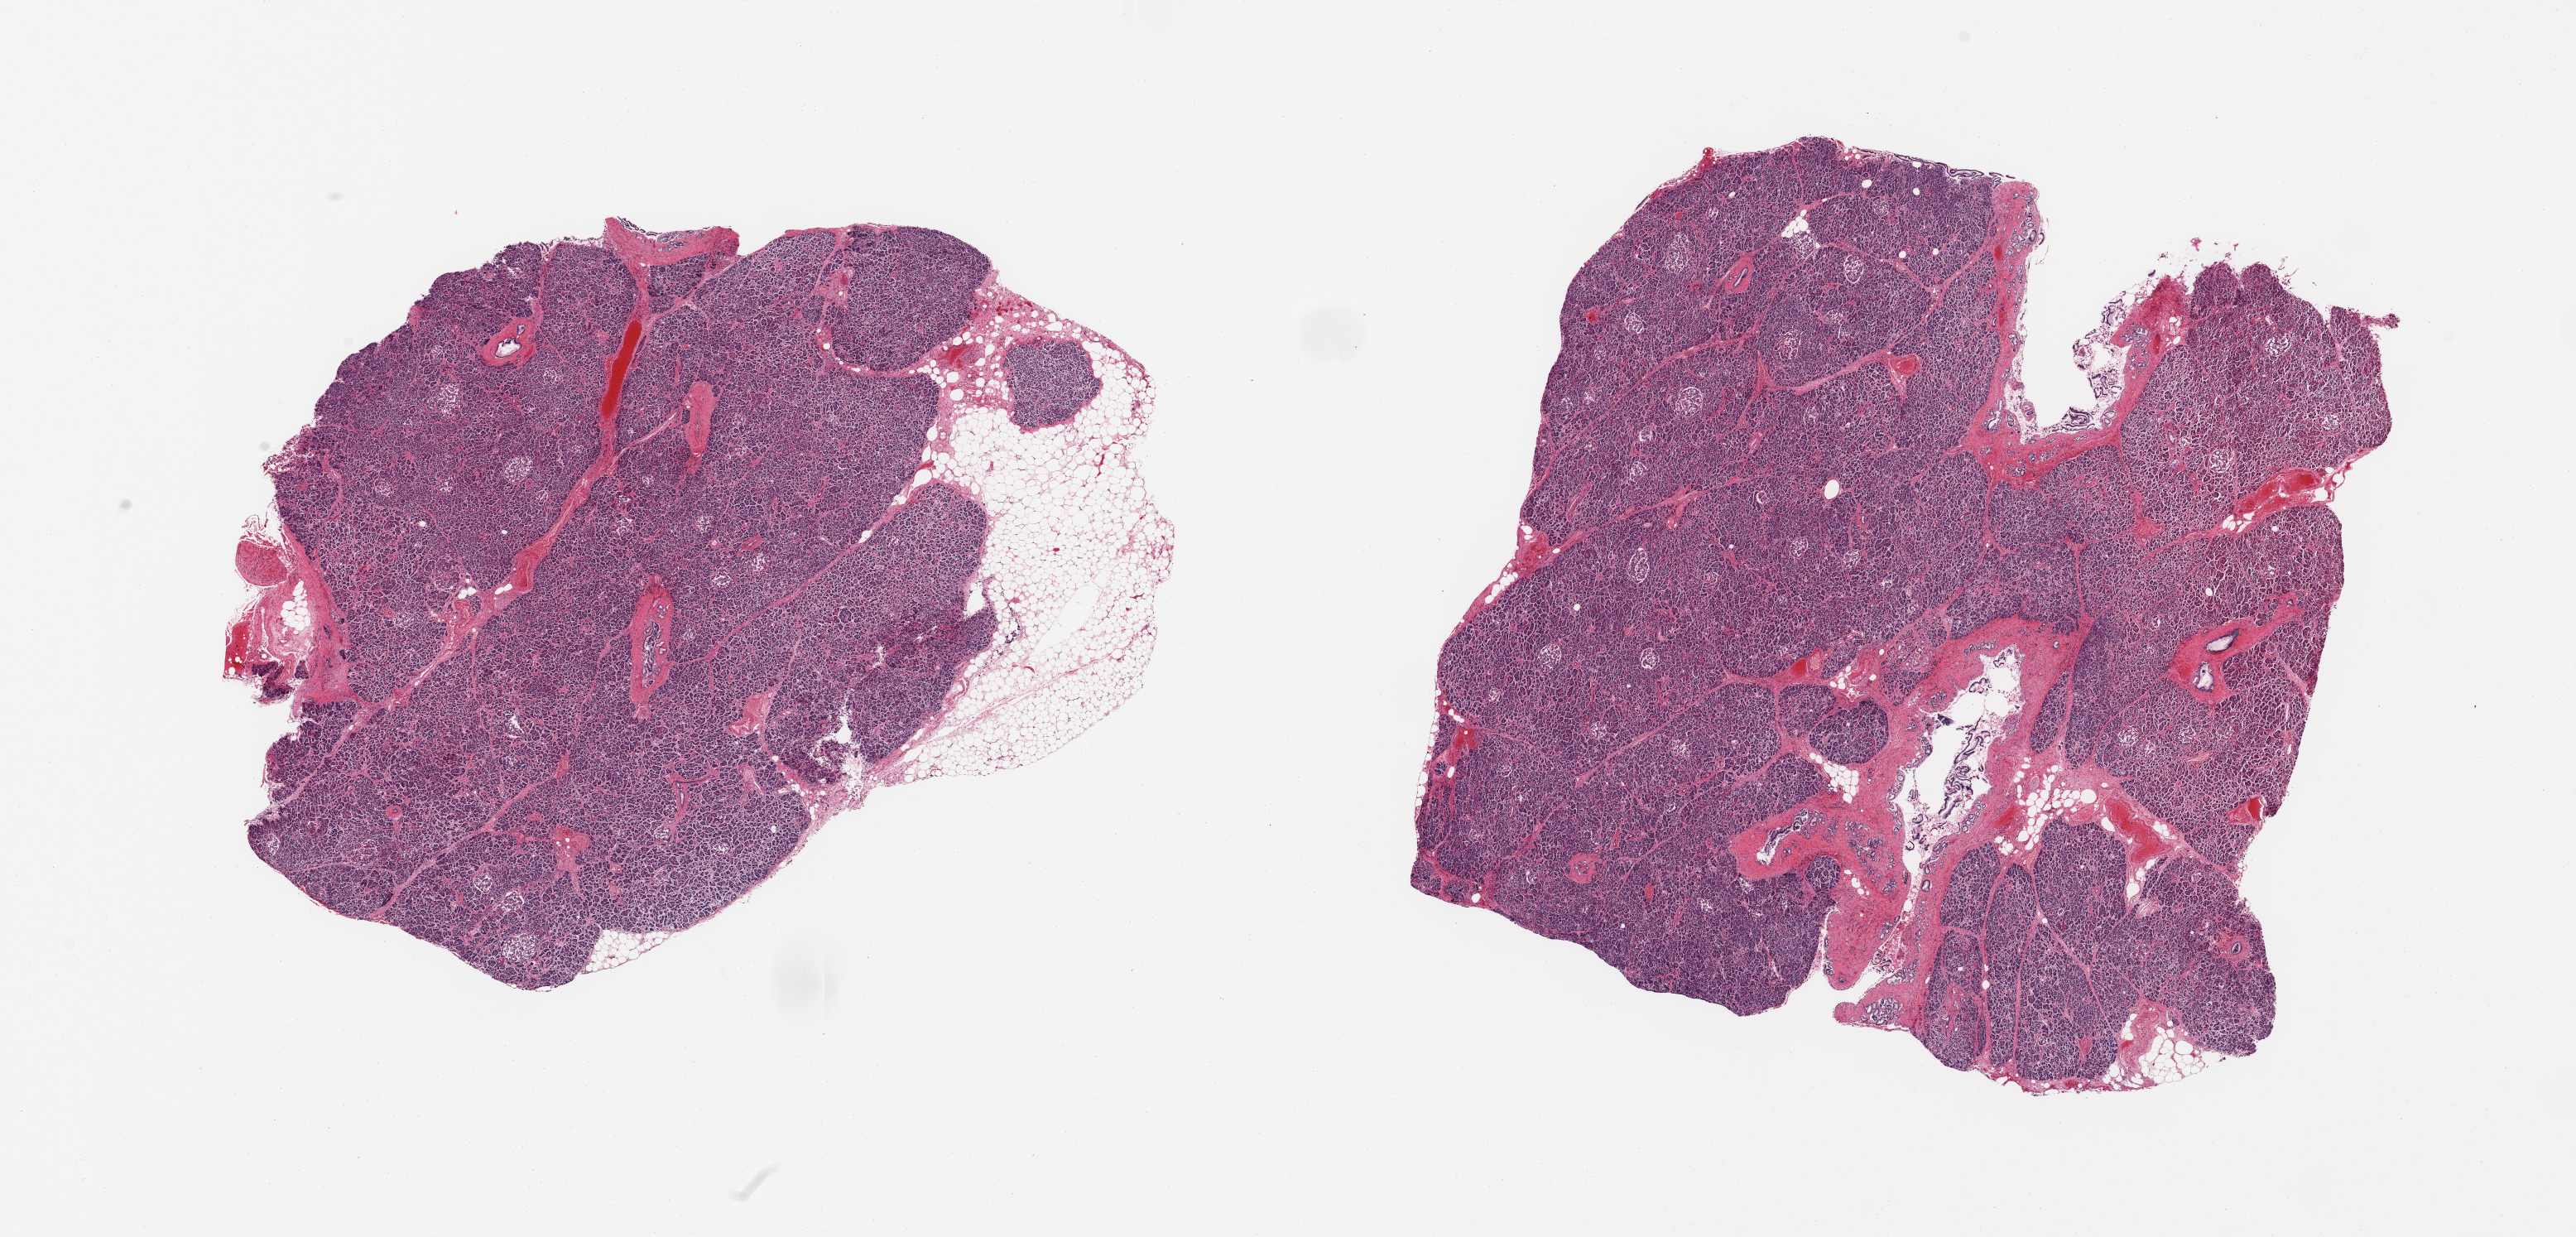
Whole-slide image, H&E stain, low-resolution overview of the scanned area, about 24.6 x 11.8 mm. PAXgene-fixed, paraffin-embedded tissue. Section of pancreas (target tissue). Tissue donor sample.
Reviewer comment on this tissue sample: 2 pieces; 20% external fat on 1 piece; large ducts in 1 piece; suspicious for PanIN 1, but too autolyzed to be certain.